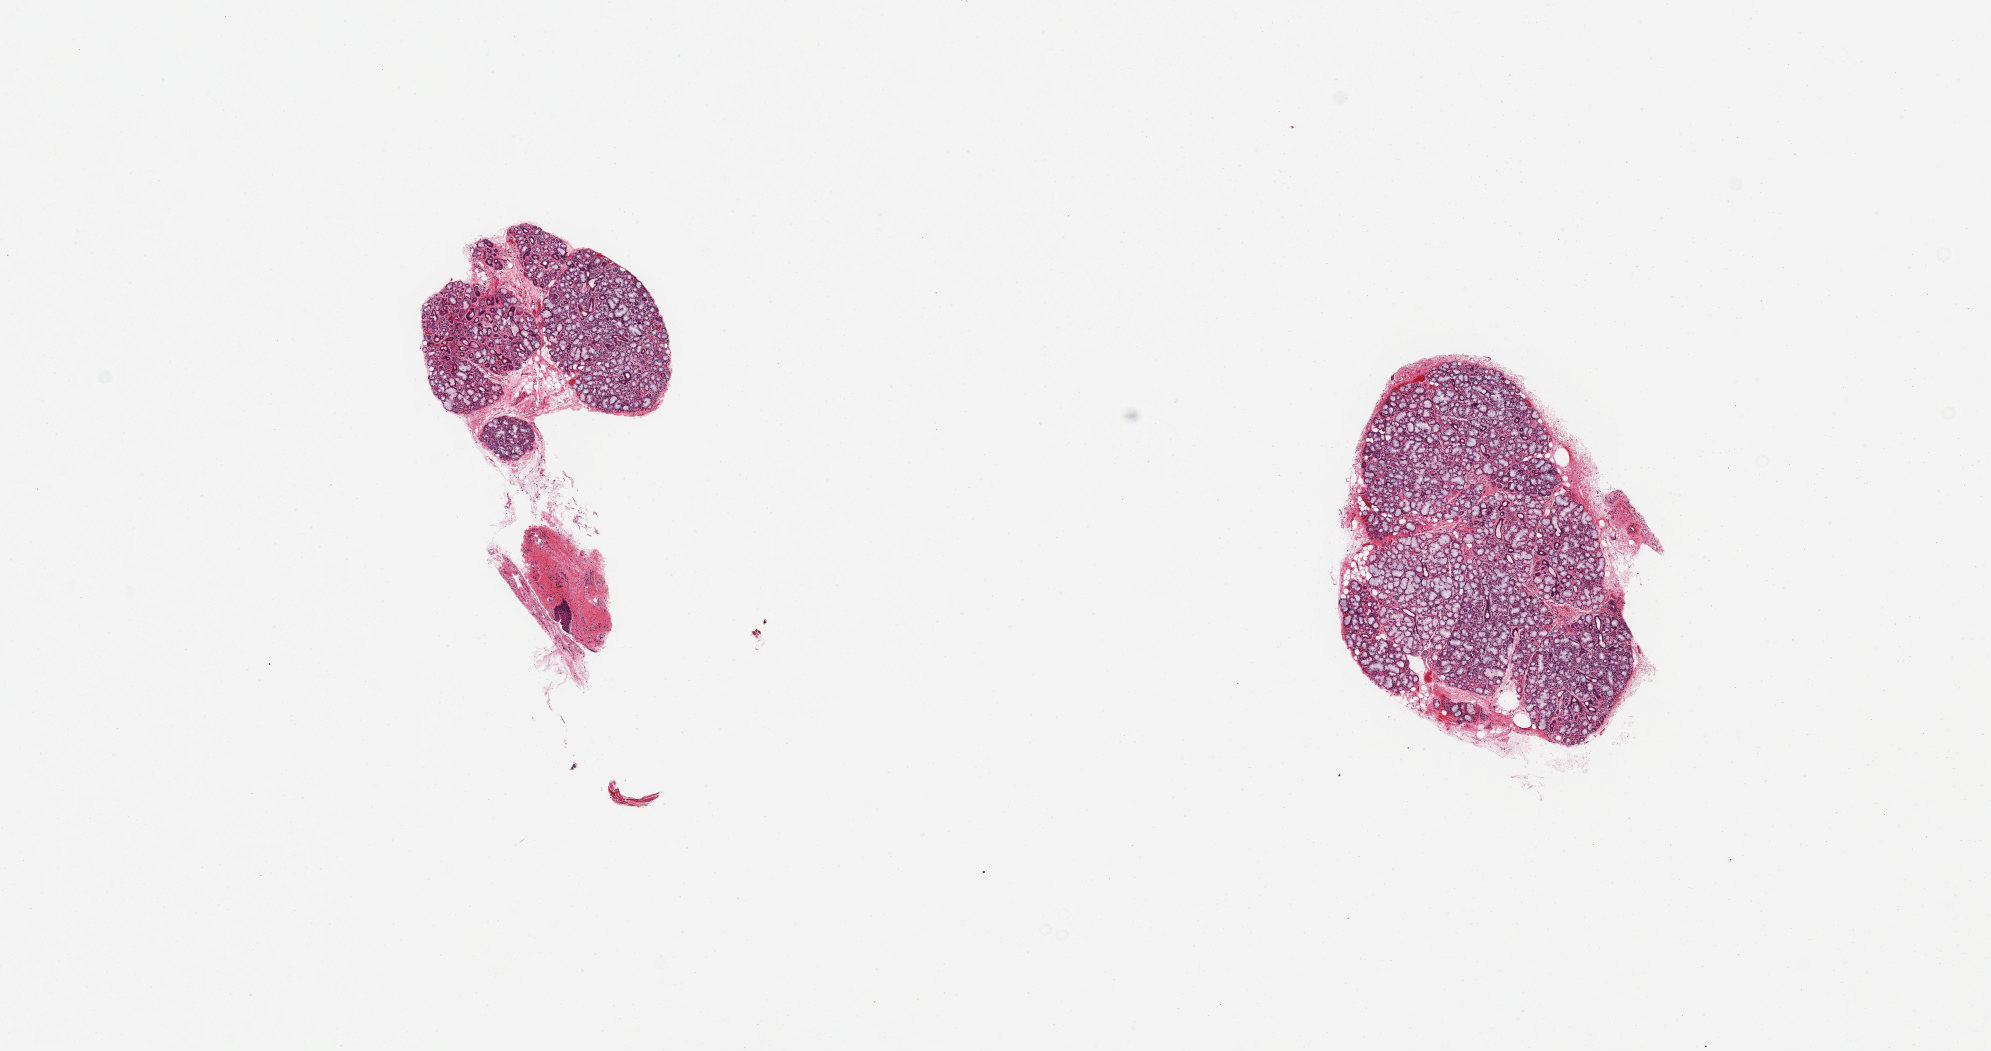
H&E whole-slide image — shown as a low-resolution overview of the whole scanned area (about 15.8 x 8.3 mm). PAXgene-fixed paraffin-embedded (PFPE) section. Sampled site (target tissue): minor salivary gland. Donor tissue sample.
Pathologist's review note for this sample: 2 pieces; excellent specimen, mild chronic inflammation, small fragment of lip/stroma.